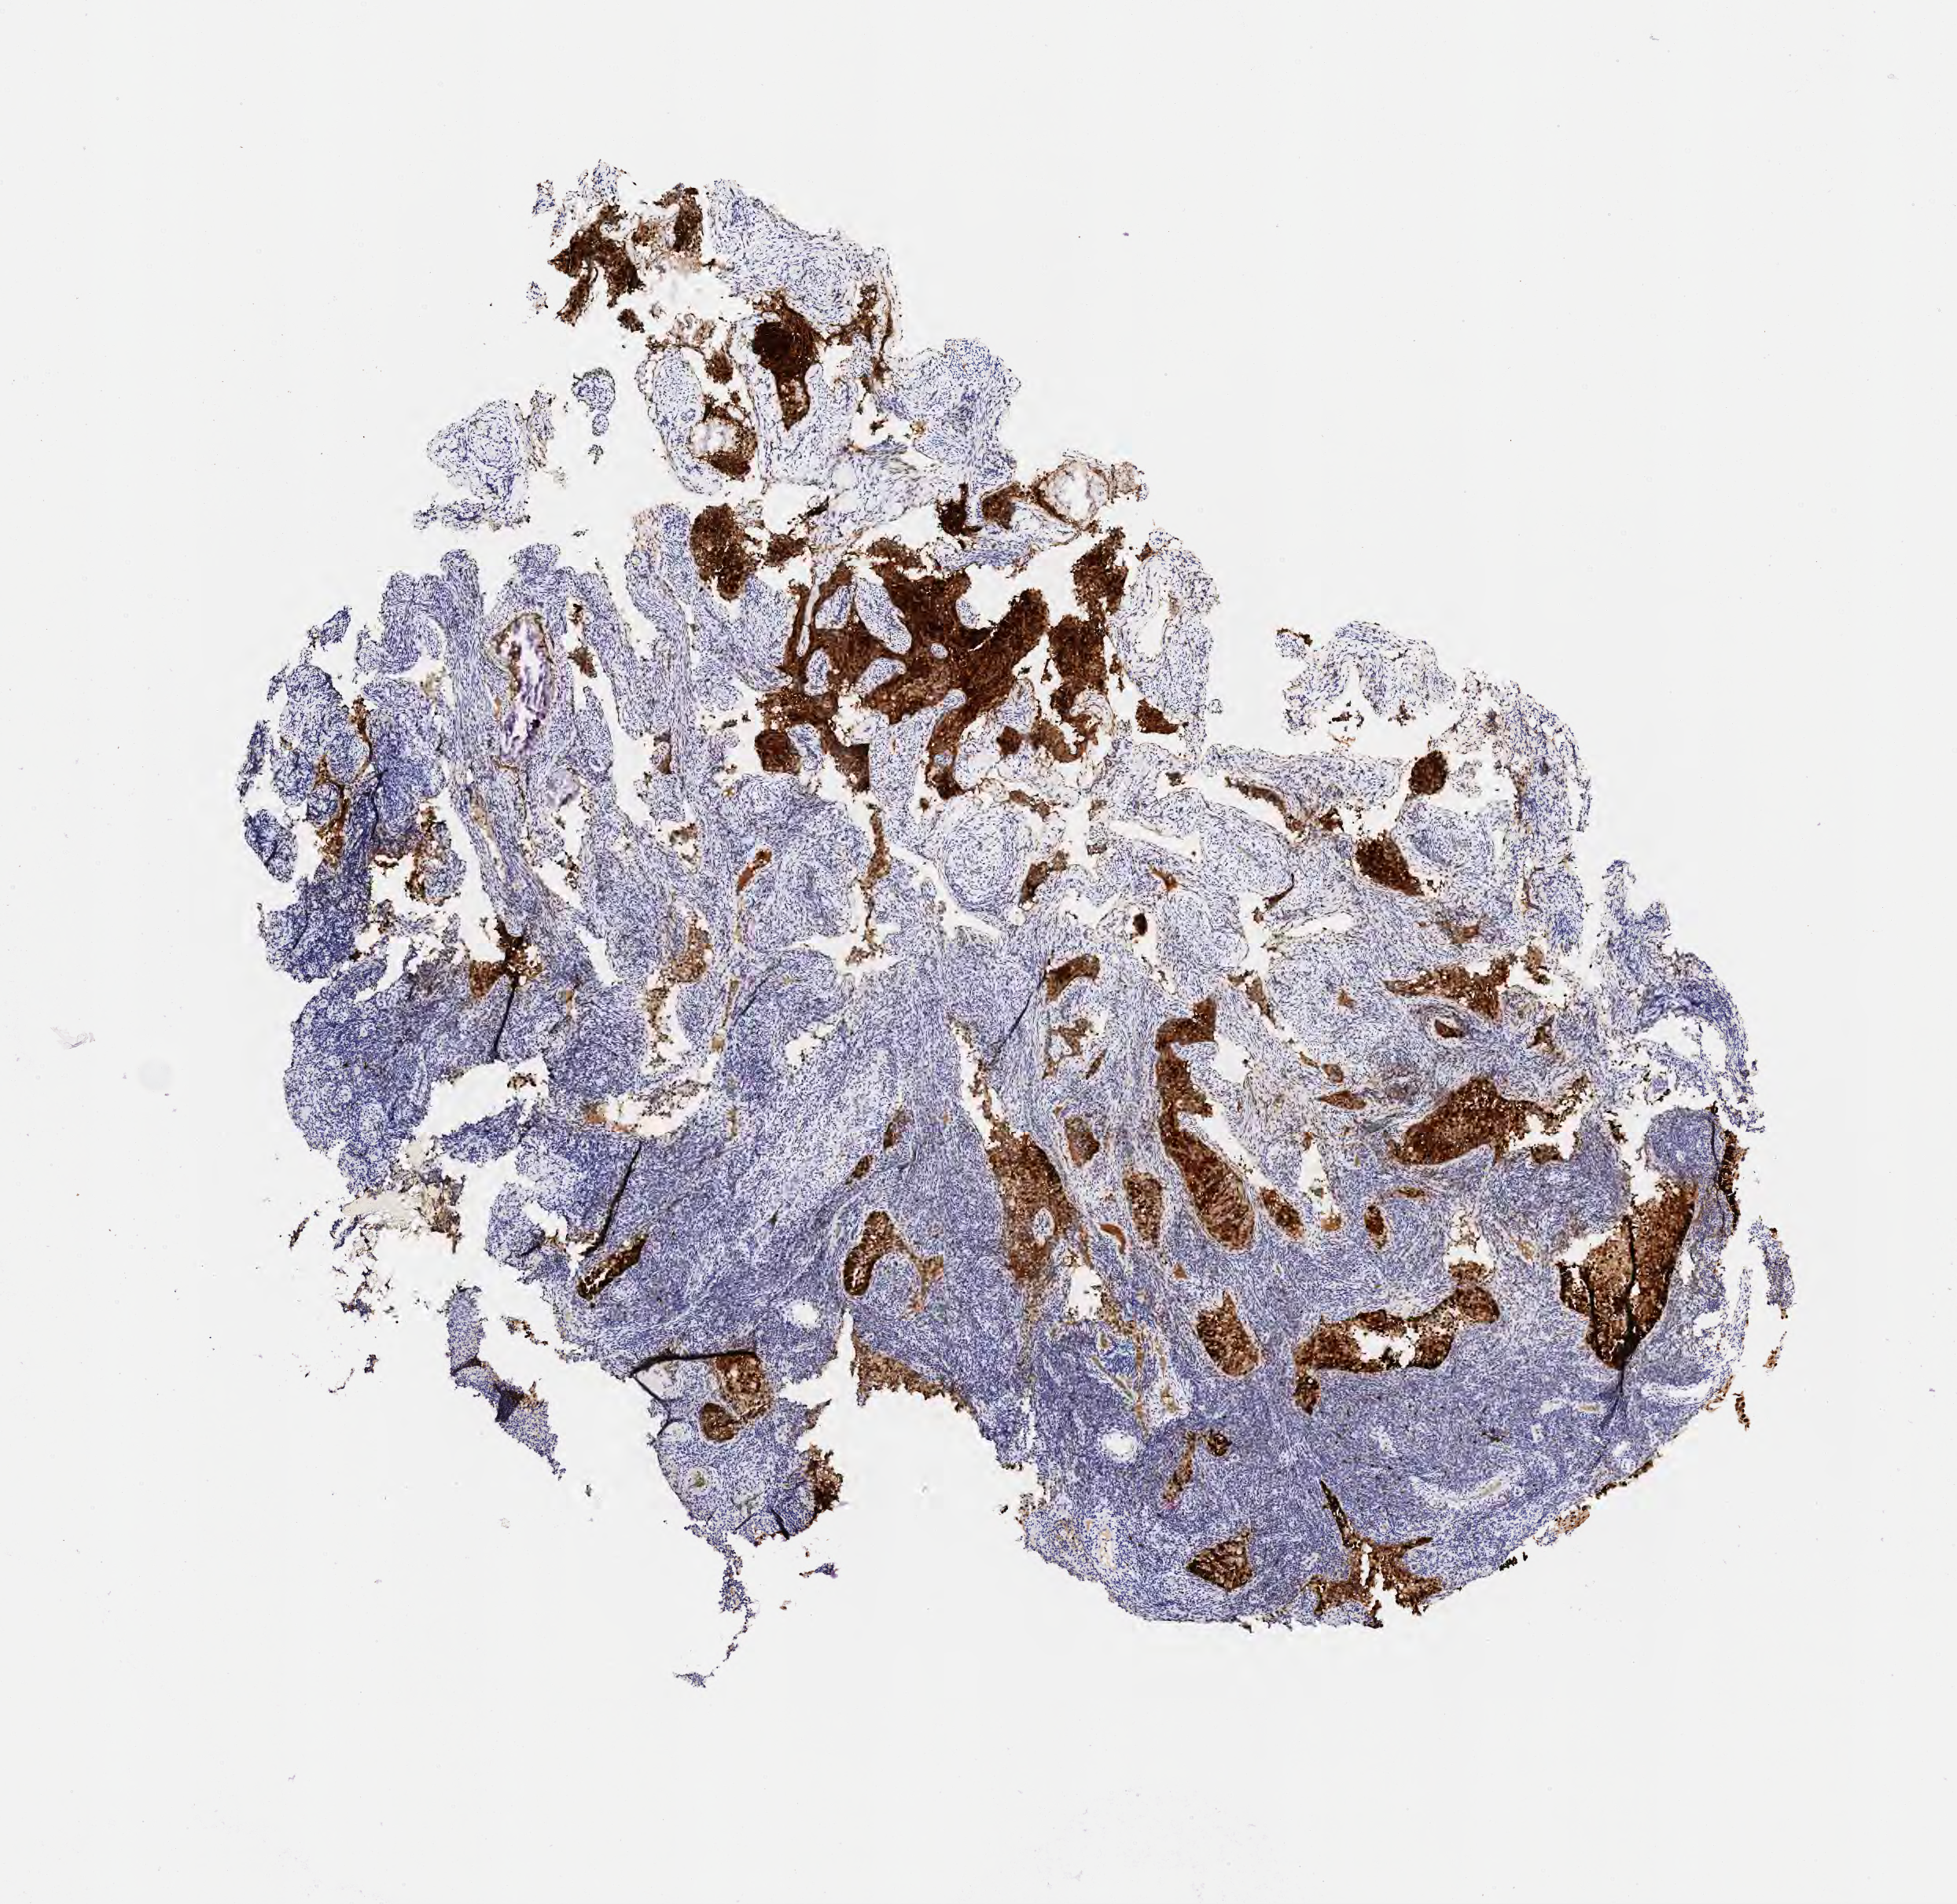
IHC for p16 (p16INK4a), whole-slide image, whole scanned area (about 5.0 x 4.9 mm) shown as a low-resolution overview. Tumor tissue. Site: cervix. Female patient, age 48 years.
Histologic diagnosis: Squamous cell carcinoma, large cell, nonkeratinizing, NOS.